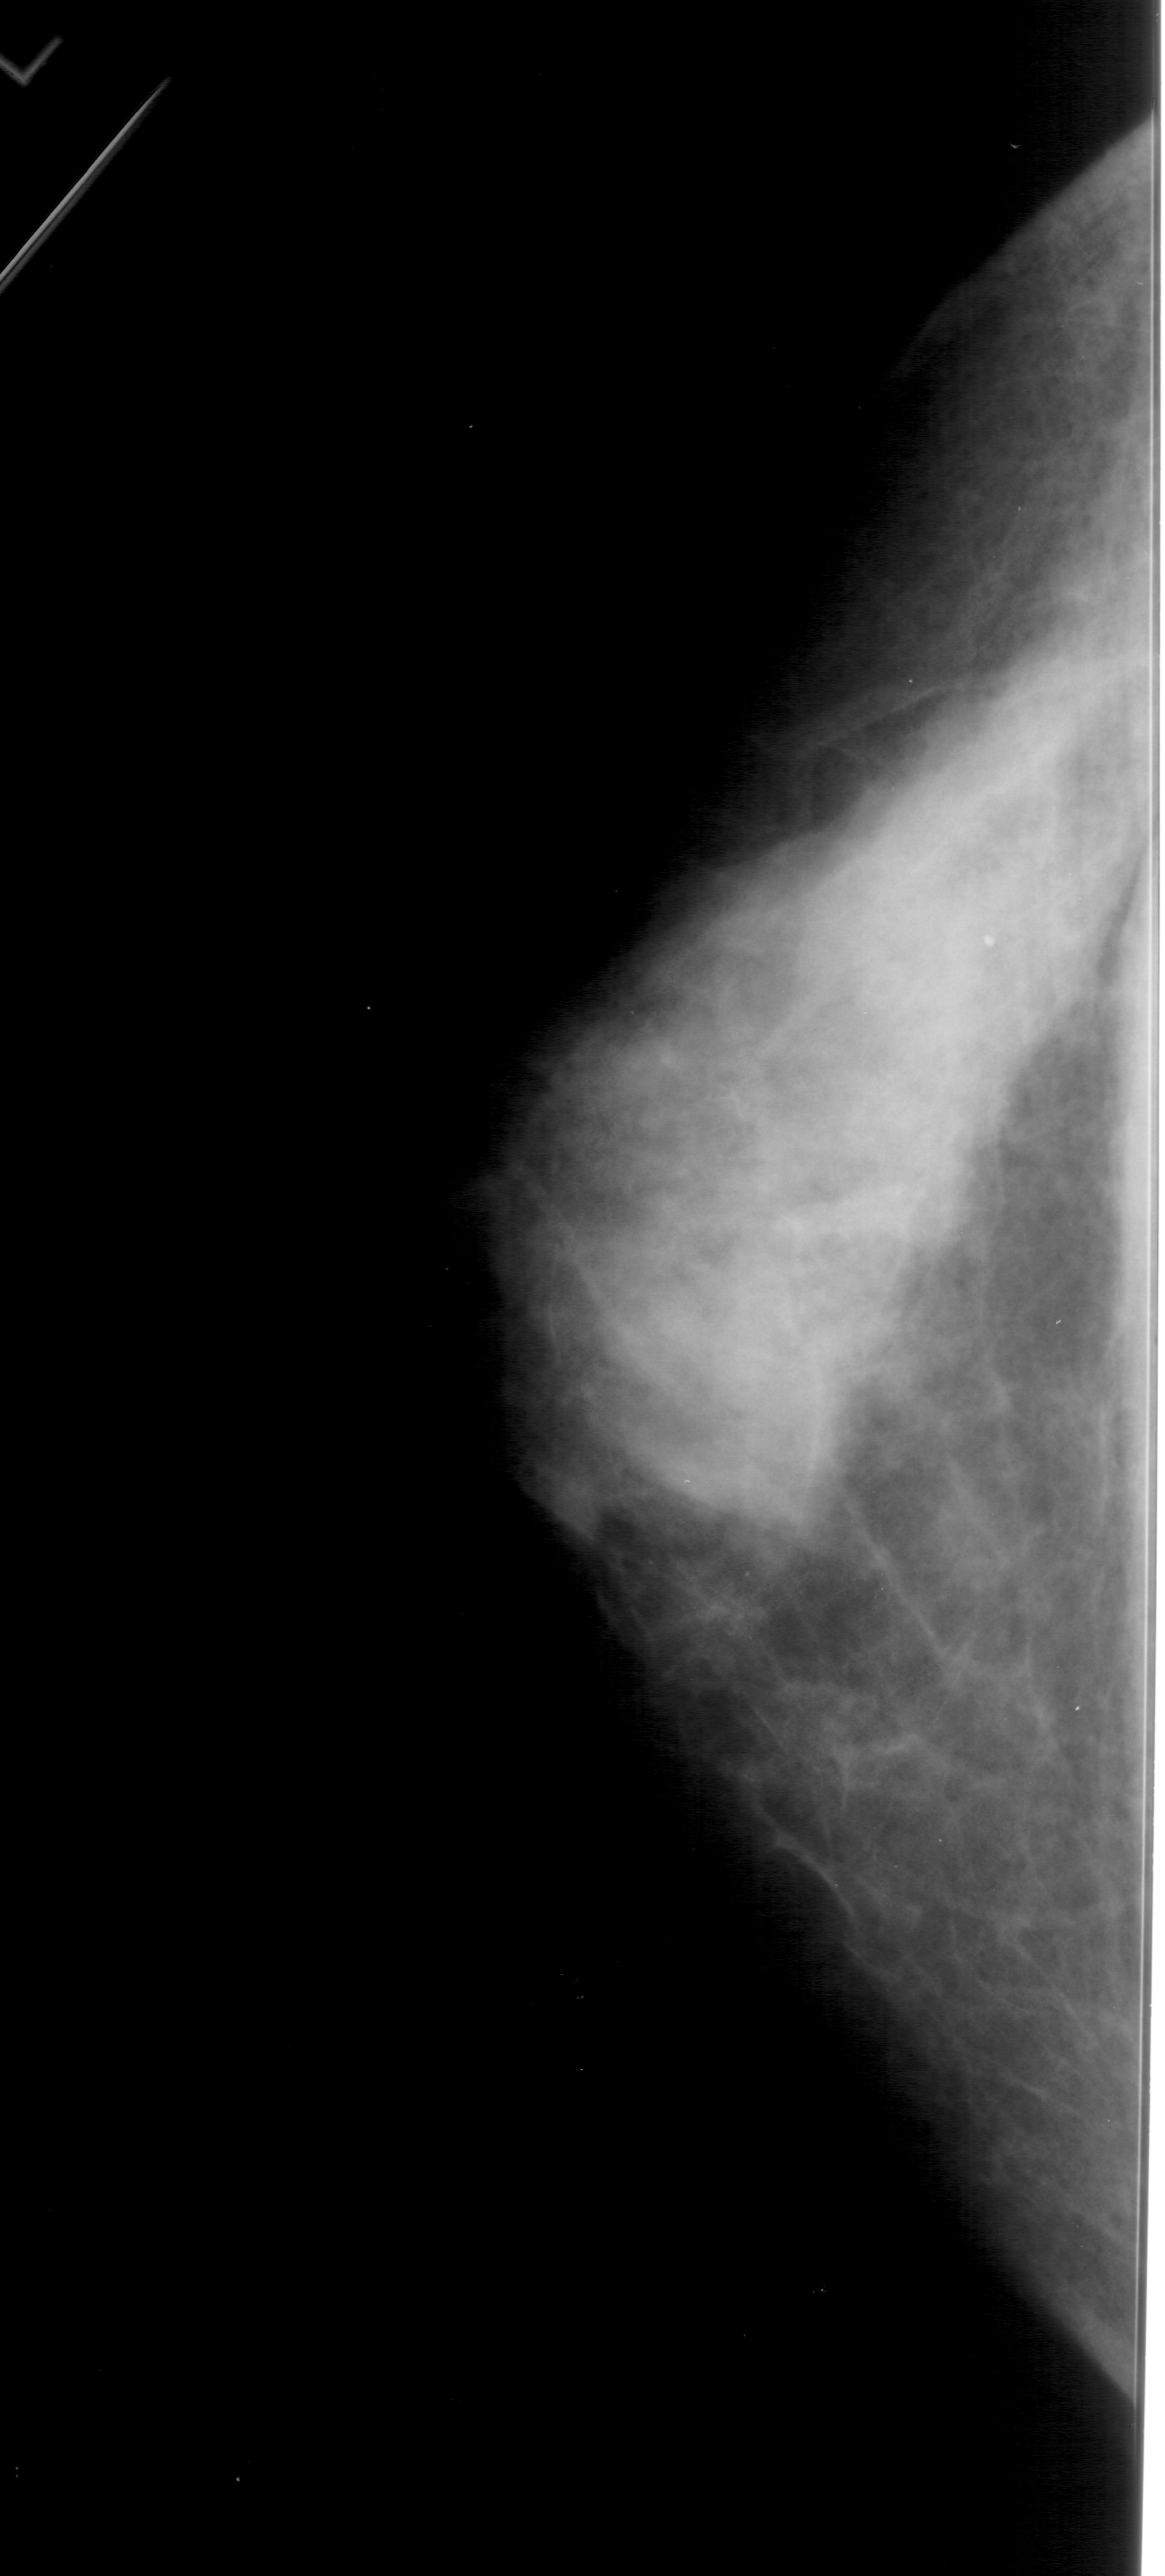
Digitized screen-film mammogram, left breast, CC view, breast composition: extremely dense (BI-RADS density category 4 of 4).
Radiologist-marked abnormalities on this image: calcifications, morphology amorphous, distribution clustered; BI-RADS assessment category 4; pathology (as recorded): benign.